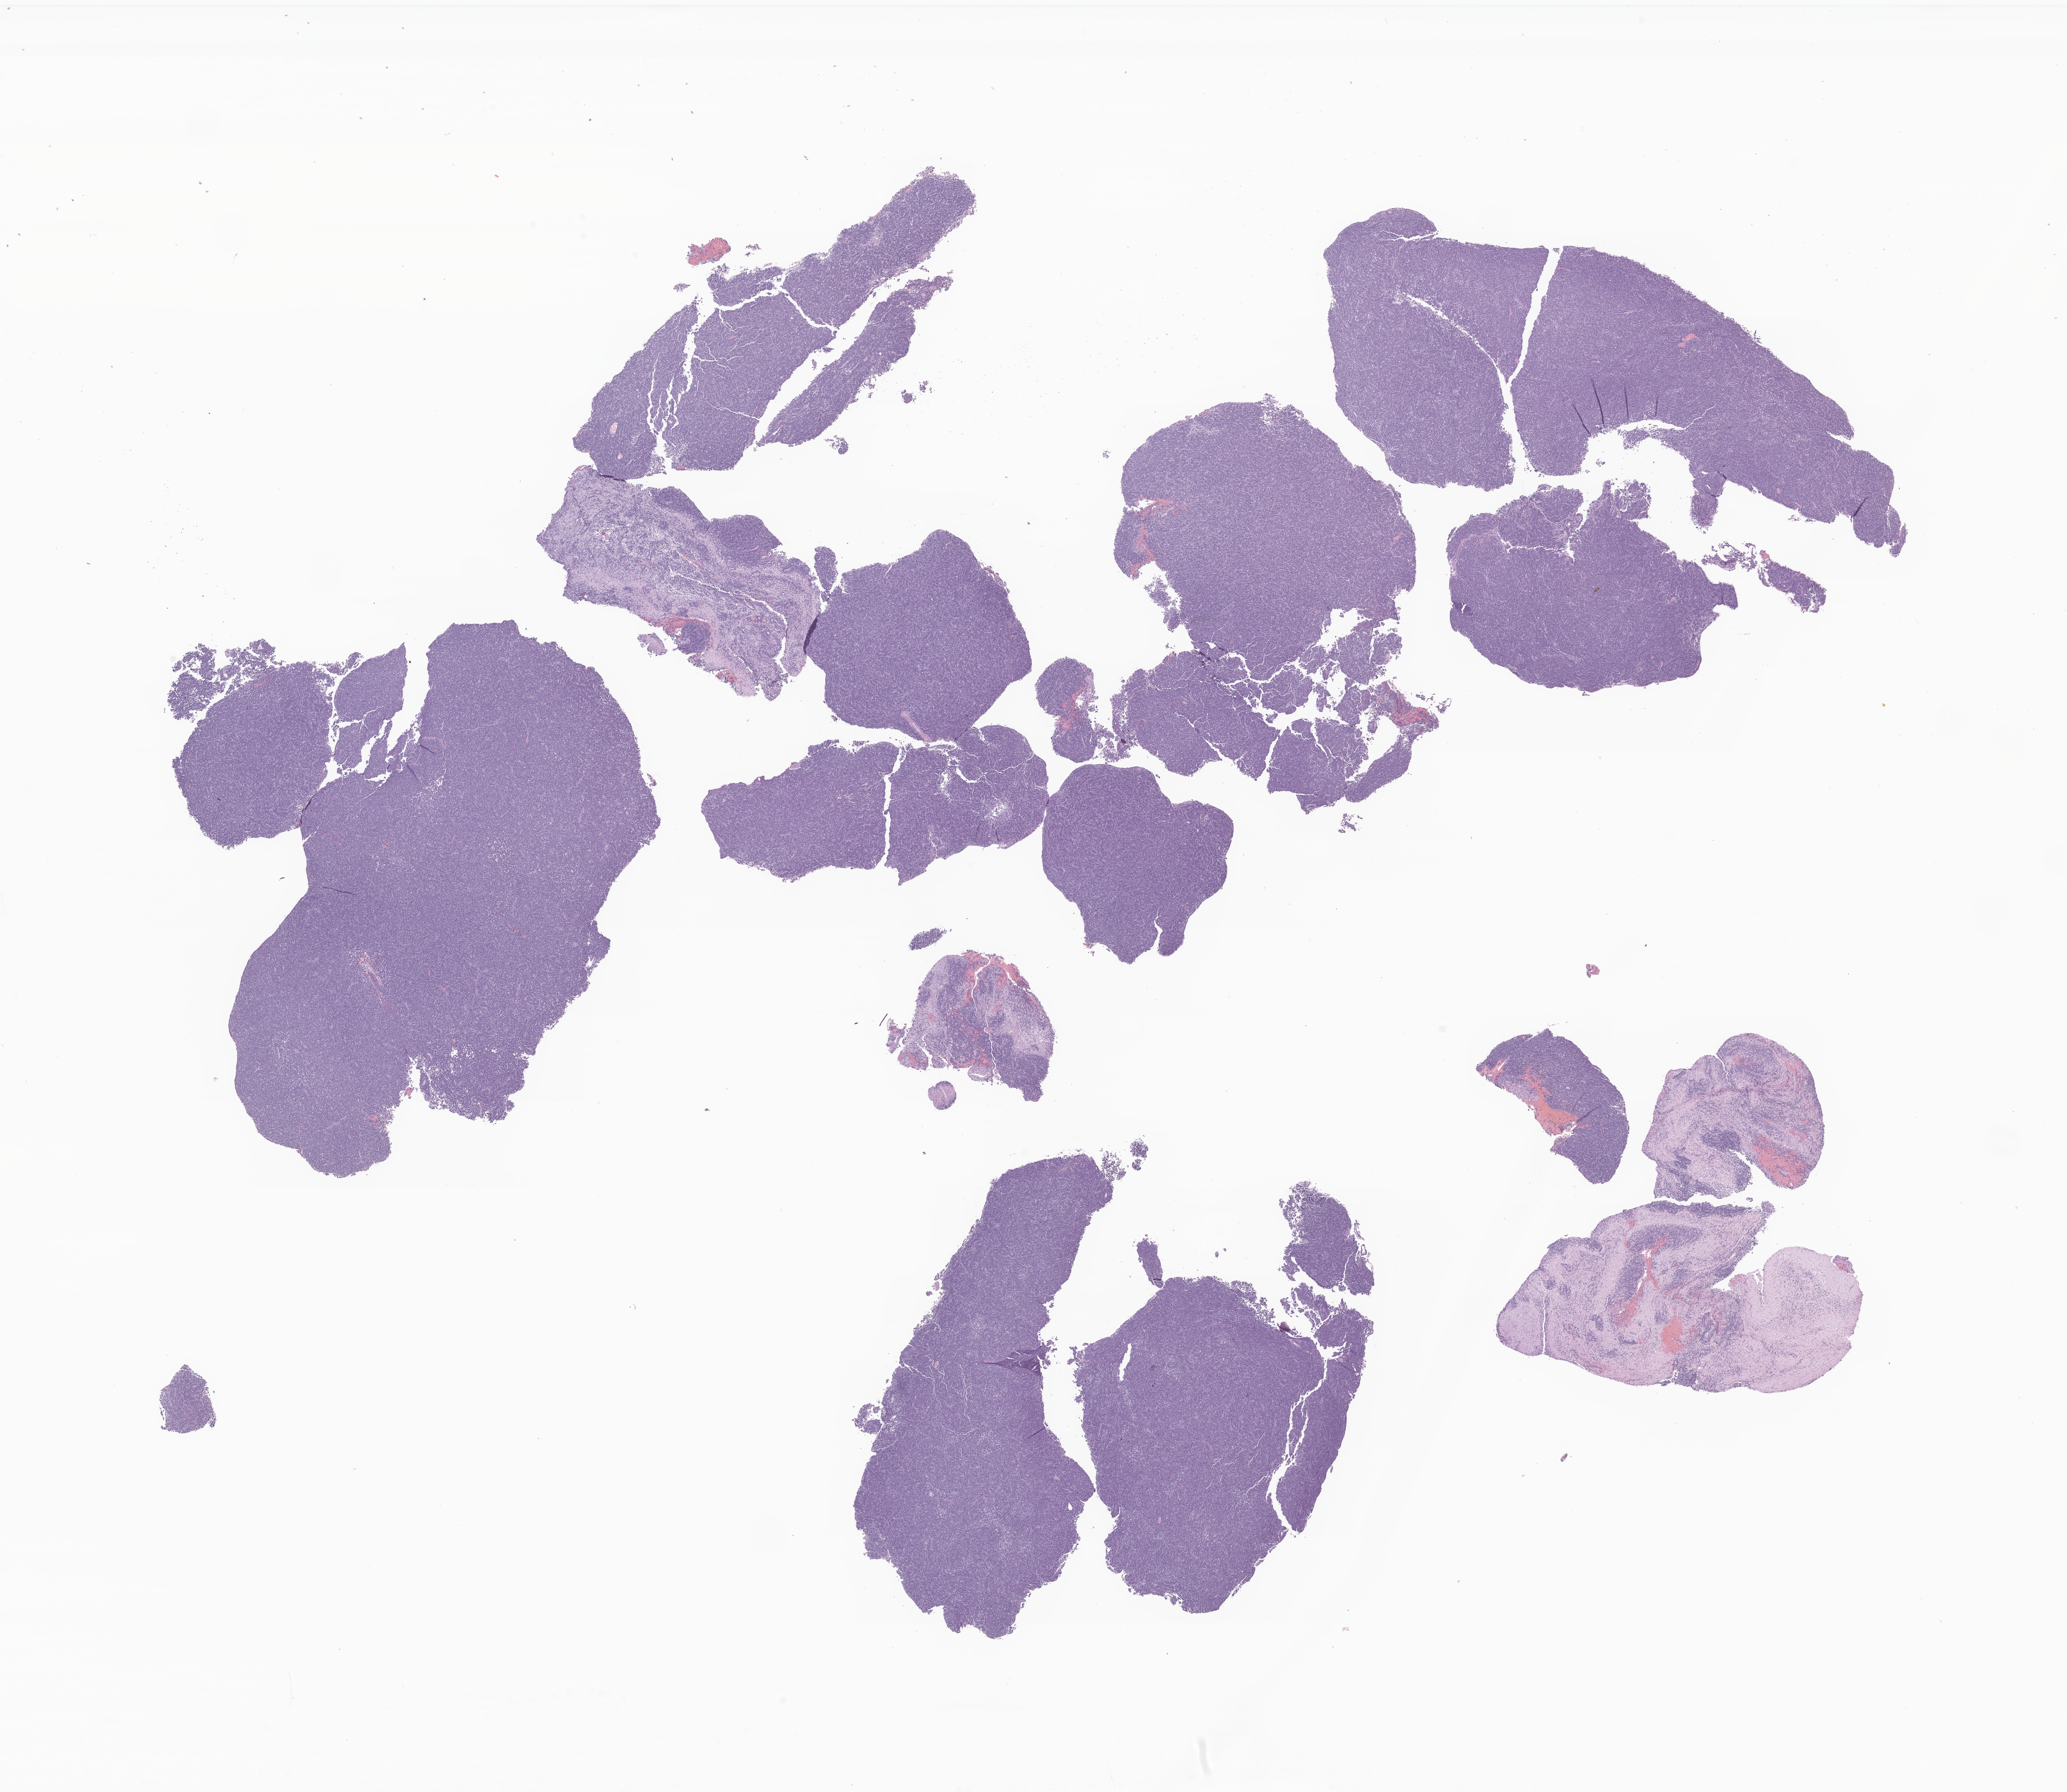
Whole-slide image, haematoxylin and eosin stain of tumor tissue from the cerebellum, low-resolution overview of the scanned area, about 25.4 x 22.0 mm; FFPE section. Male patient, age 270 months.
Recorded diagnosis: Medulloblastoma, NOS.